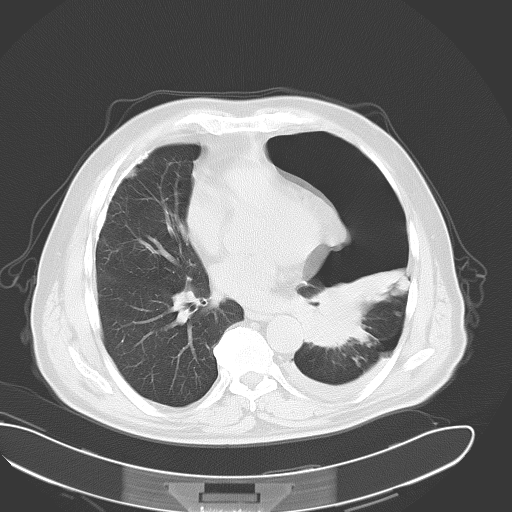
Chest CT, one axial slice. Slice 21 of 43 in the series (ordered by position). Reconstruction kernel B70f. Lung window (W 1500 / L -600 HU). 8 mm slice thickness. 512 × 512 image matrix. Male patient, age 62 years. Case-level facts recorded for this patient, not image findings: clinical TNM (as recorded): T3 N0 M1.
Outlined on this slice (rectangle marked by the reading radiologist):
- lung tumour (recorded histology: adenocarcinoma): bounding box (x1, y1, x2, y2) in pixels: (304, 284, 377, 349)
- lung tumour (recorded histology: adenocarcinoma): (304, 289, 372, 353)